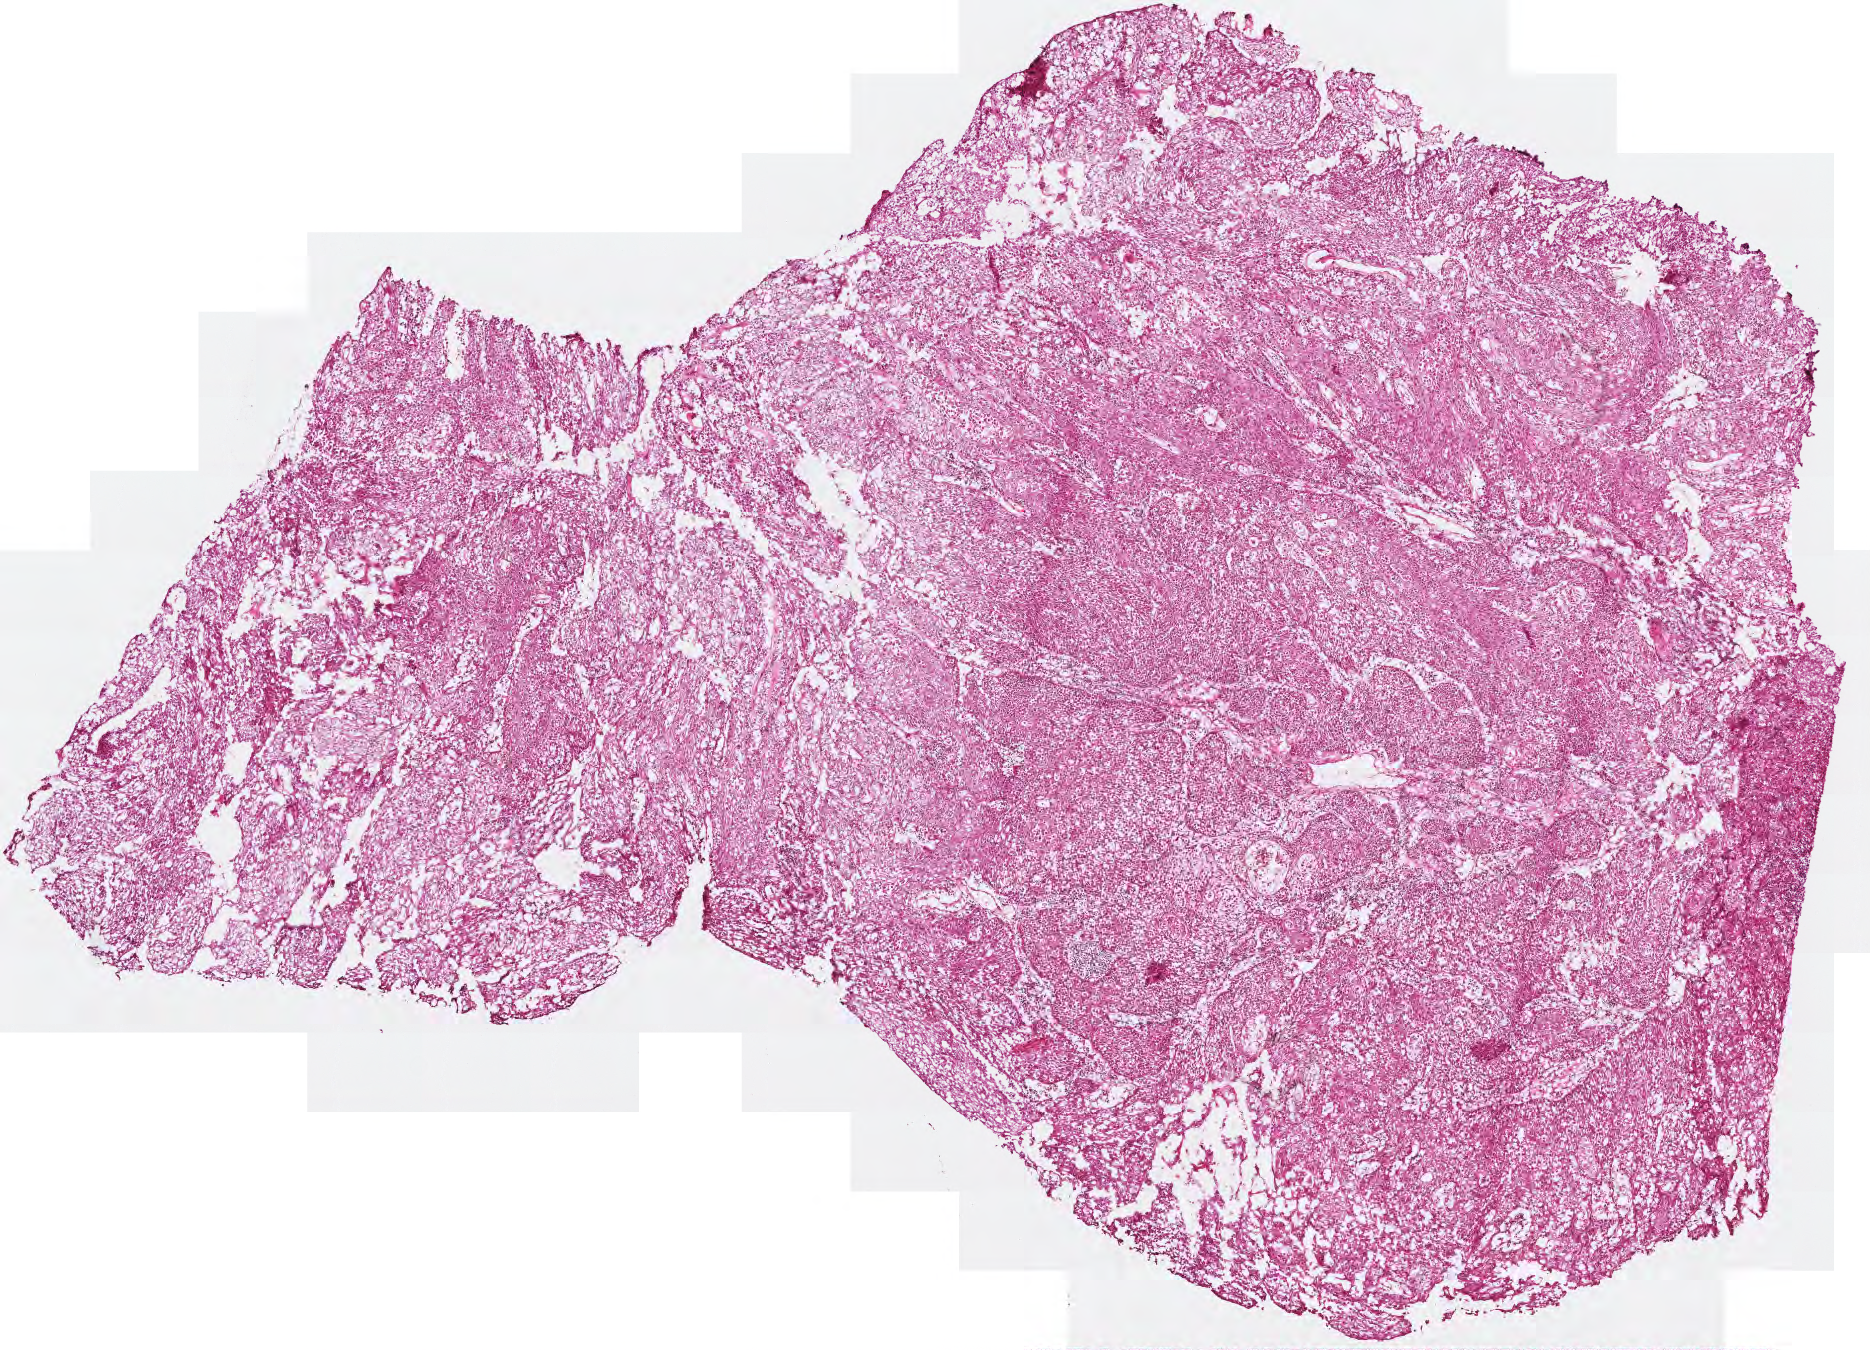
Digitized H&E tissue section (whole slide) — whole scanned area (about 3.7 x 2.7 mm) shown as a low-resolution overview, frozen section from the top of the tissue portion, sample: primary tumour, head and neck. Male, age 53 years at initial diagnosis.
Diagnosis: Squamous cell carcinoma, NOS (tonsil, NOS).